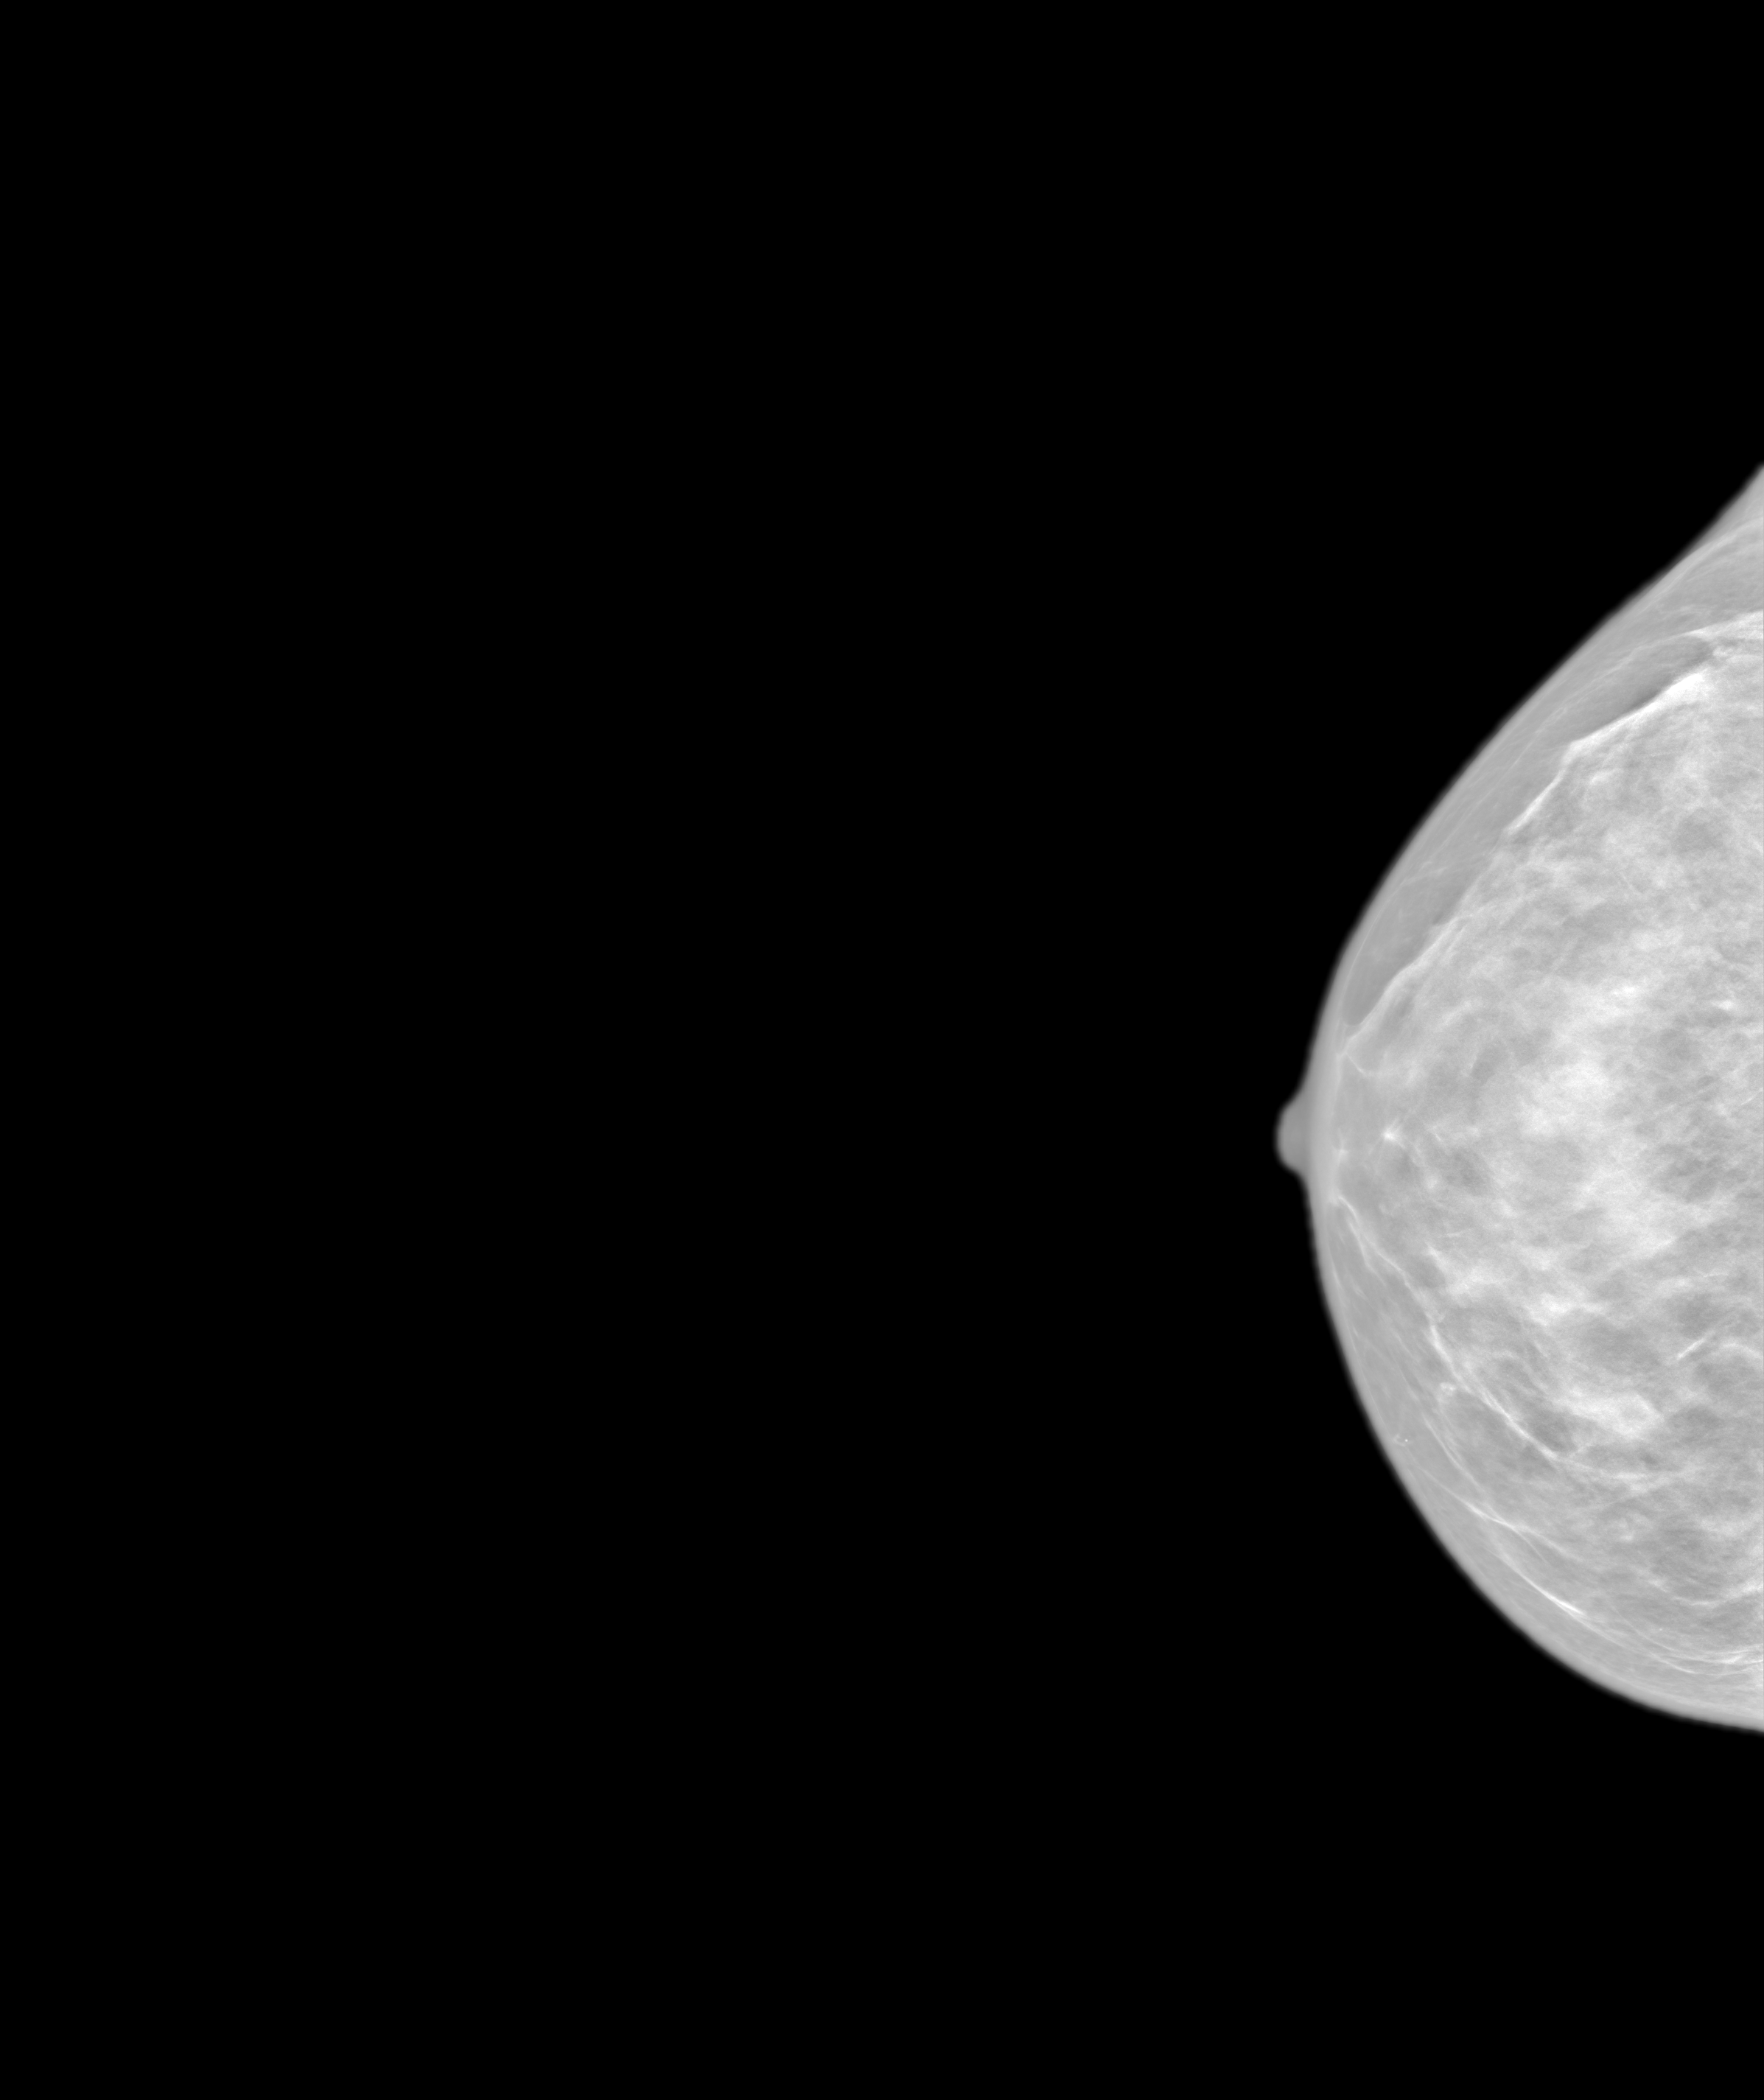
Annual screening mammography examination. Patient aged 44 years (female).
Image type: synthesized 2-D view from tomosynthesis. Breast: right. Projection: cranio-caudal projection.